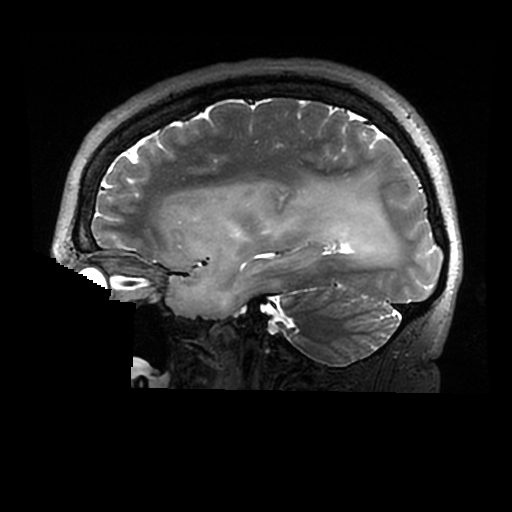
Brain MRI from a brain-tumour surgery series, one sagittal slice. Slice 199 of 320 in the series (ordered by position). 0.6 mm slice thickness. 512 × 512 image matrix, field of view 240 × 240 mm. From the clinical record (not read from this slice): histopathology: Astrocytoma; WHO grade: 2; IDH mutation: yes.
Outlined on this slice (outlined manually by an expert reader):
- tumour: bounding box <167,181,400,319> (left, top, right, bottom; pixels)